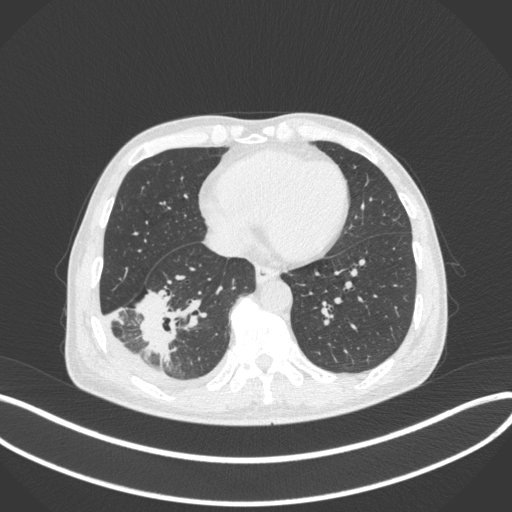
Chest CT, one axial slice. Reconstruction kernel B31f. 120 kVp. Lung window (W 1500 / L -600 HU). 1 mm slice thickness. 512 × 512 image matrix, field of view 400 × 400 mm. Male patient, age 64 years. Case-level facts recorded for this patient, not image findings: clinical TNM (as recorded): T3 N0 M0.
Annotated regions visible in this slice (bounding box drawn by a radiologist):
- lung tumour (recorded histology: adenocarcinoma): box from (x=133, y=283) to (x=183, y=369) px